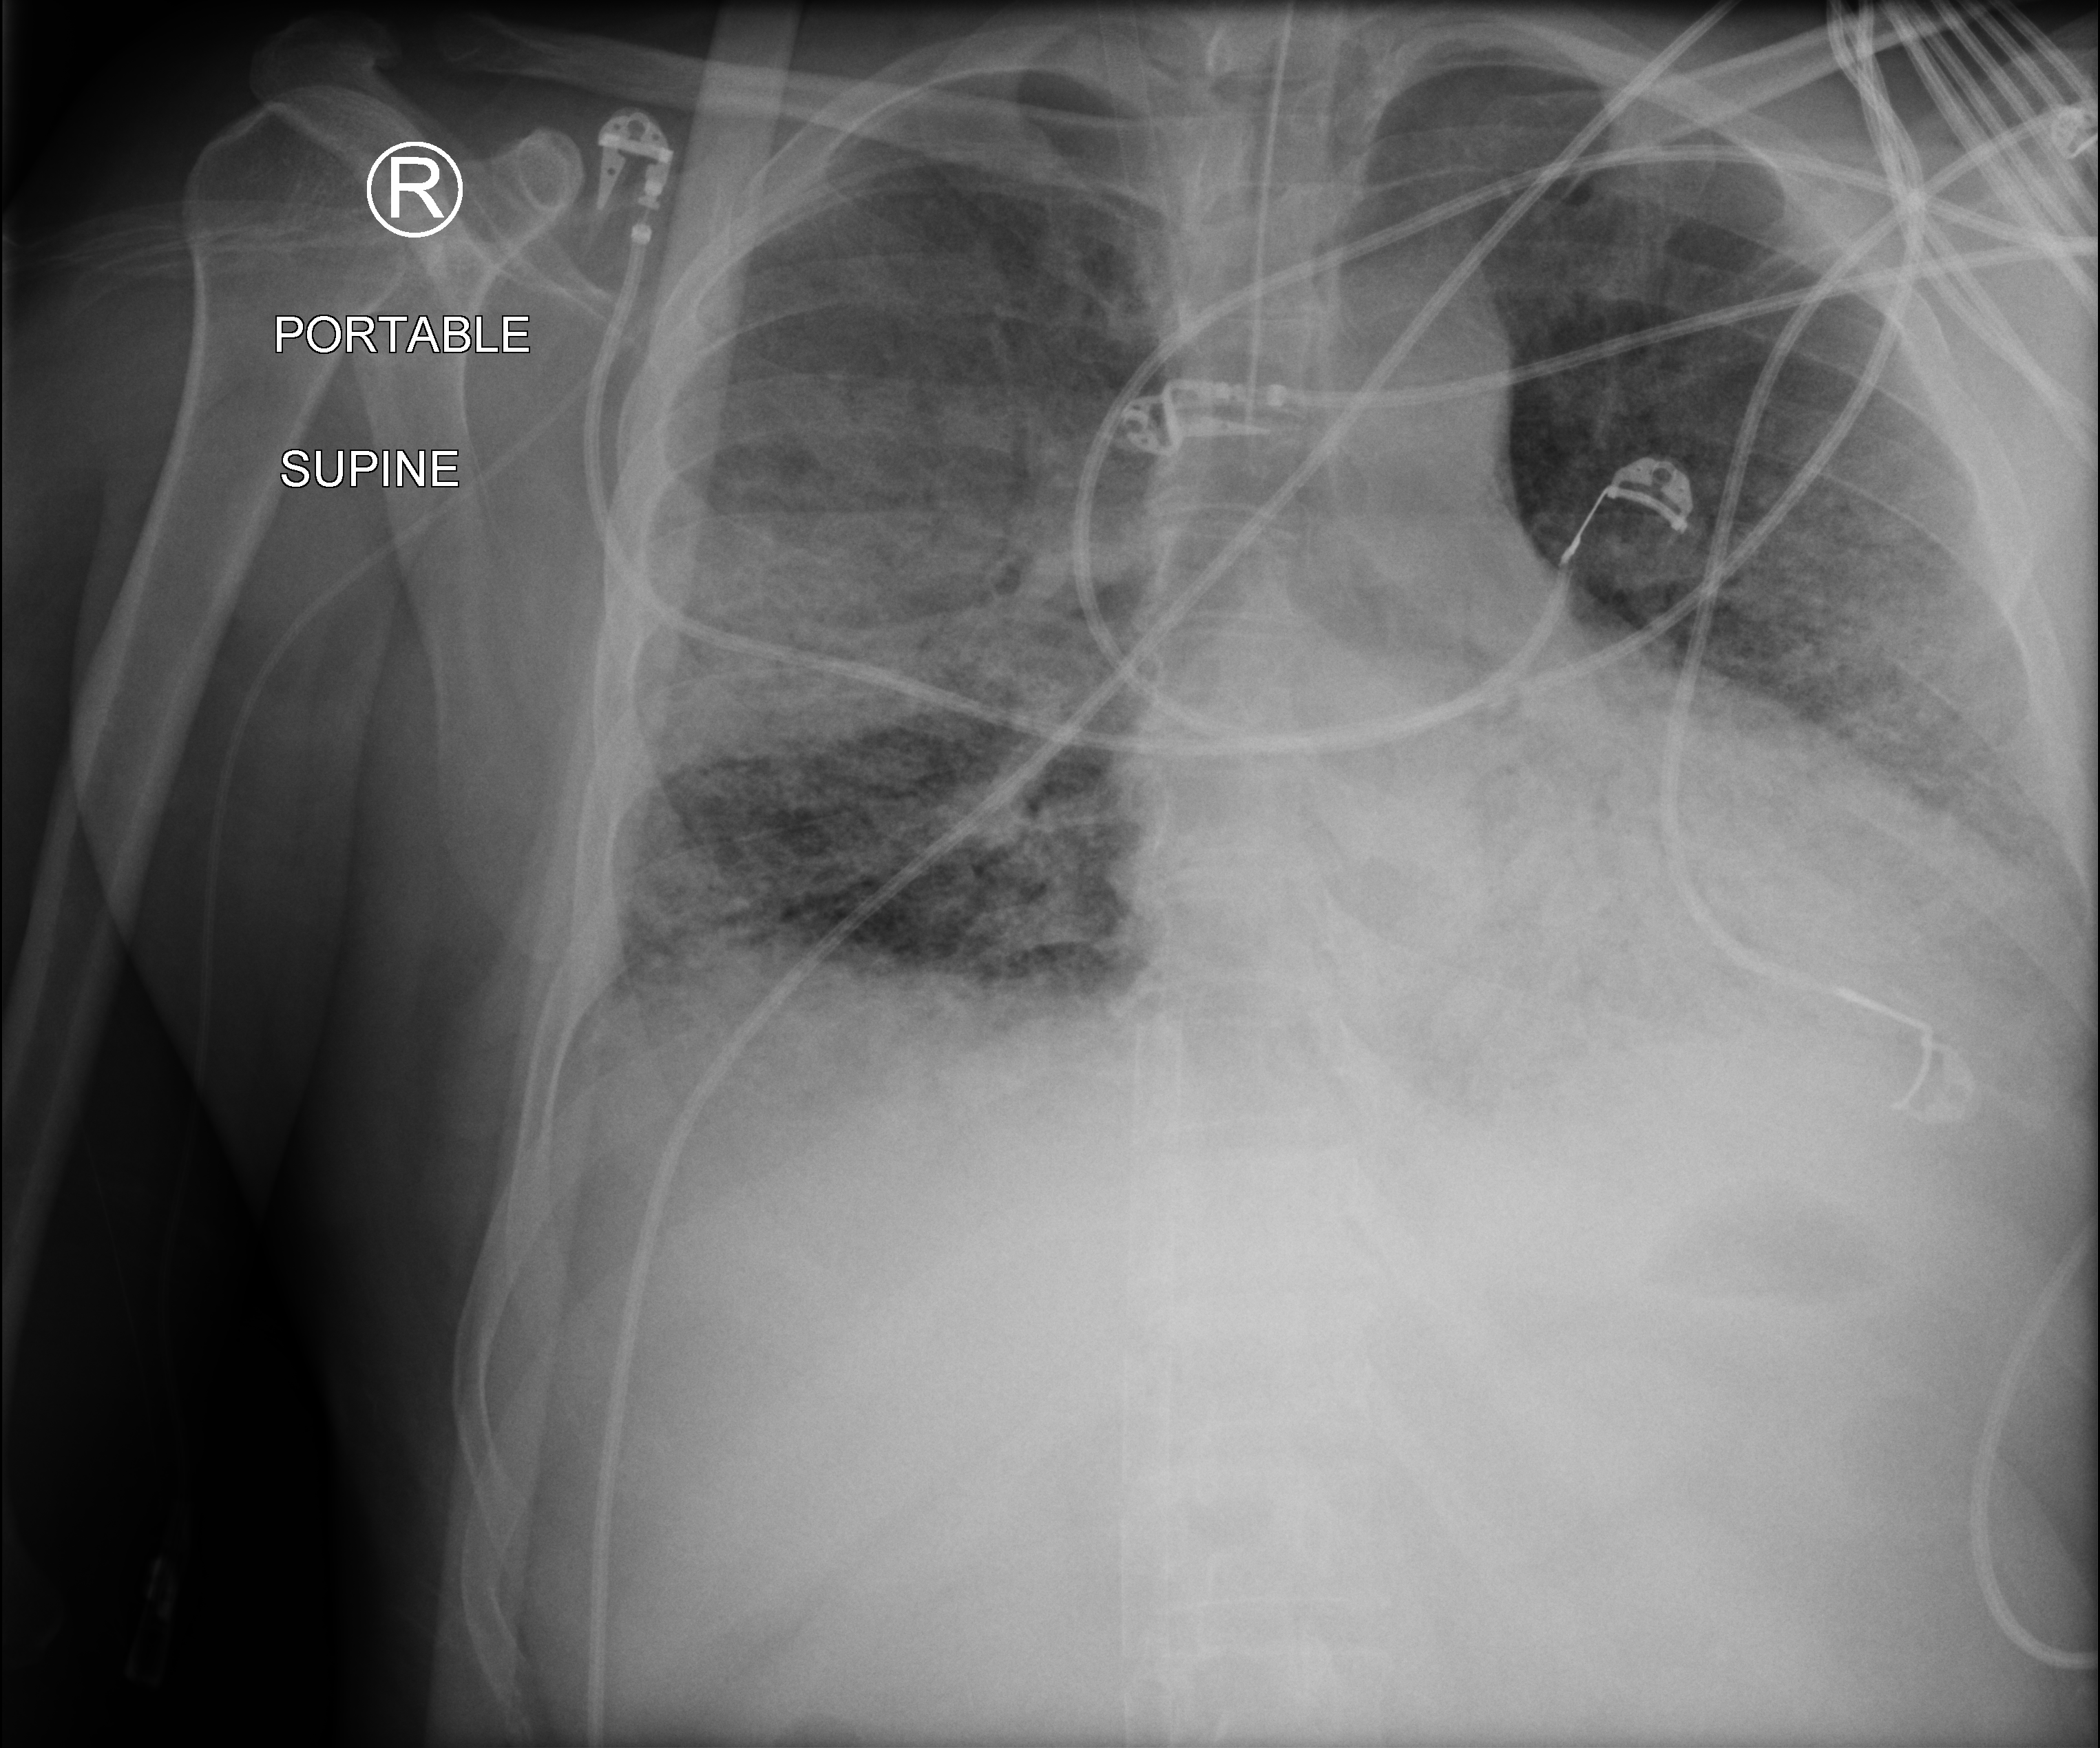
Portable chest radiograph; anteroposterior (AP) projection. Patient hospitalised with COVID-19; male, aged 18–59 years.
From the hospital-stay record, not from the radiograph (when in the stay this image was taken is not recorded): mechanically ventilated during this hospital stay: yes; smoking status (admission record): never.